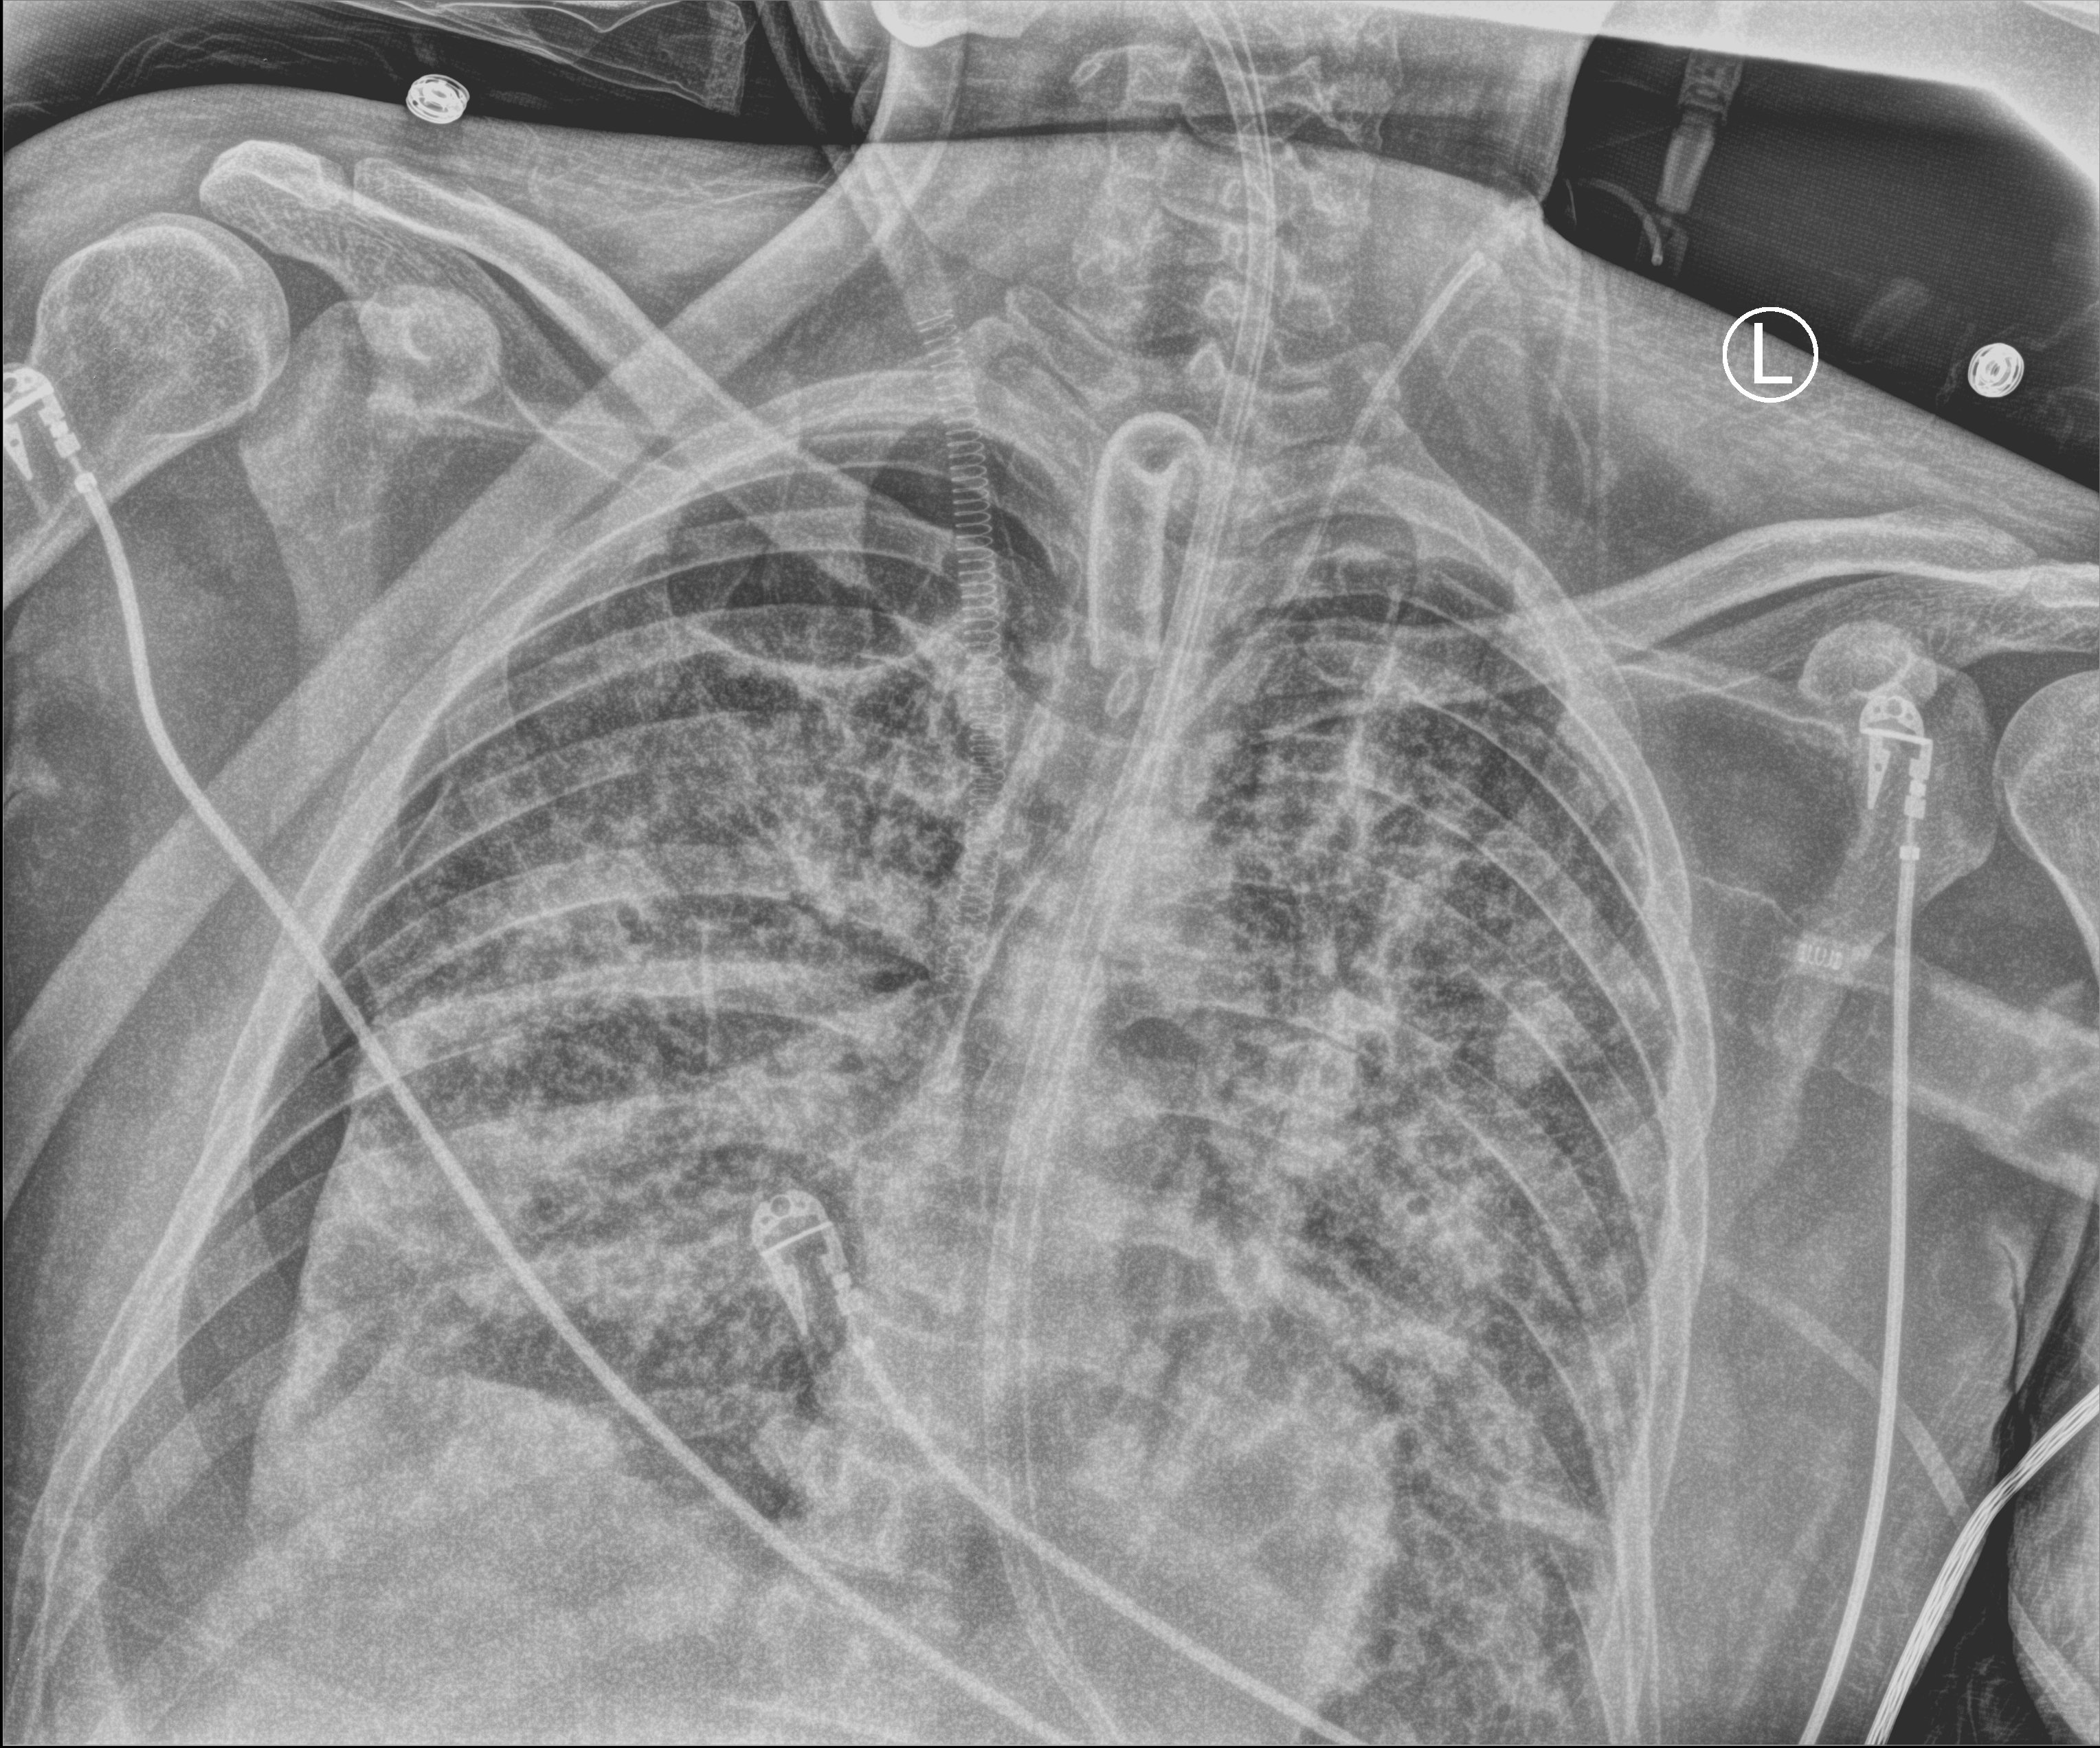
Chest X-ray (portable), anteroposterior (AP) projection. Patient hospitalised with COVID-19, aged 18–59 years.
Hospital-stay facts (about this admission, not read from this image; timing relative to this image not recorded): admitted to intensive care during this hospital stay: yes; length of hospital stay: 60 days.